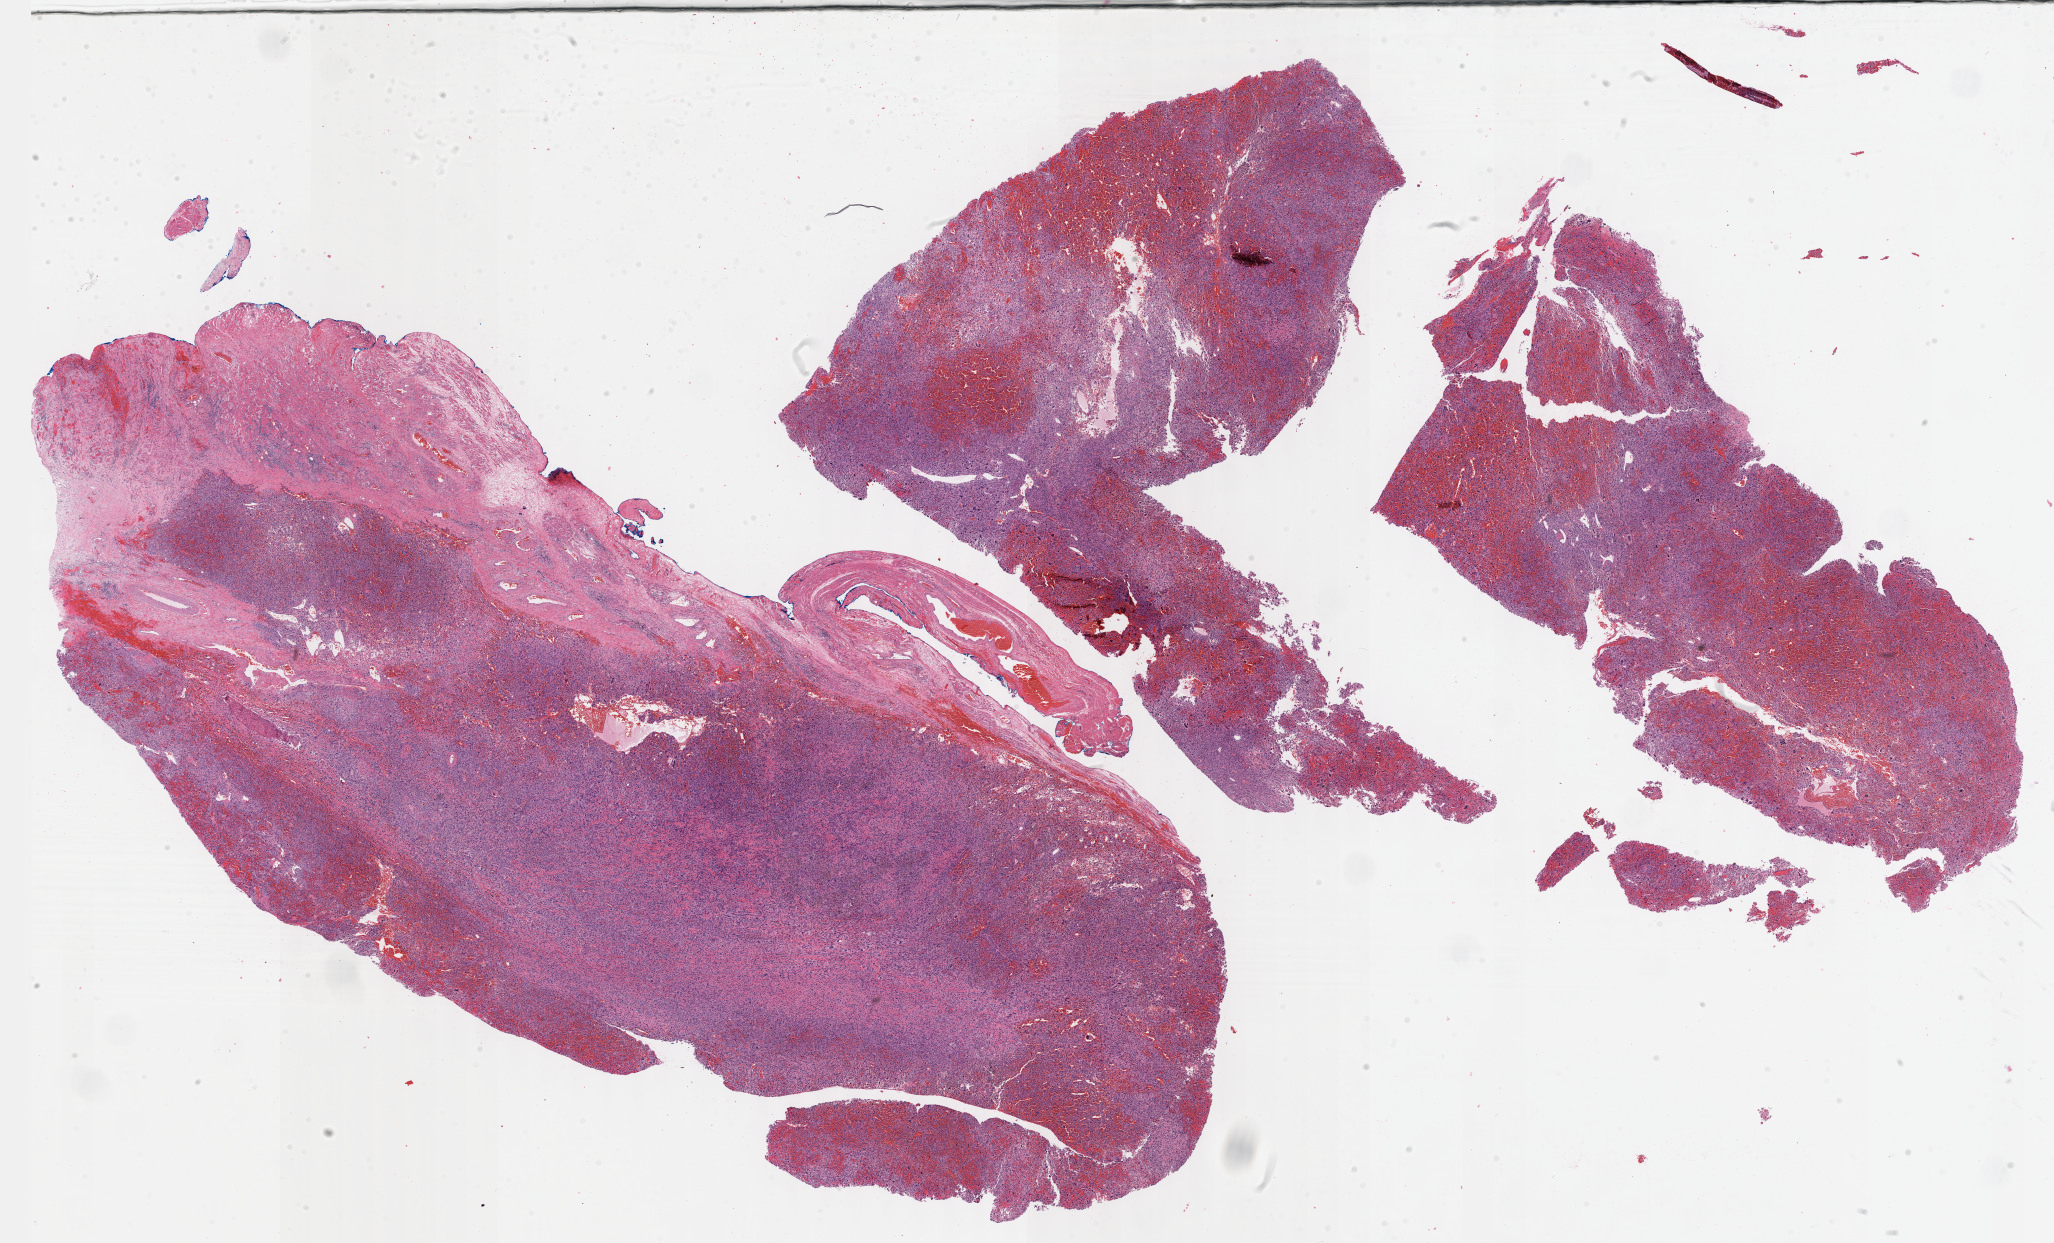
Whole-slide histology image, H&E — low-resolution overview of the scanned area, about 33.2 x 20.1 mm, formalin-fixed paraffin-embedded (FFPE) diagnostic section, primary tumour sample from the connective, subcutaneous and other soft tissues. Male patient; age at initial diagnosis 56 years.
Diagnosis: Undifferentiated sarcoma (connective, subcutaneous and other soft tissues of lower limb and hip).